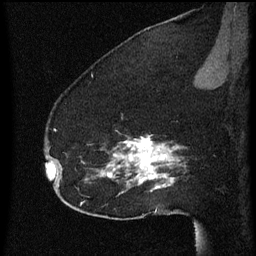
Breast MRI (dynamic contrast-enhanced), one sagittal slice. Slice 45 of 60 in the series (ordered by position). Dynamic contrast-enhanced series, image 2 of 3 at this slice position (ordered by acquisition). 1.5 T. TE 4.2 ms, TR 8 ms. 256 × 256 image matrix, field of view 180 × 180 mm. Female patient, age 52 years.
Outlined on this slice (semi-automatic segmentation, software-assisted and operator-edited):
- analysis volume of interest (the breast-tissue region the enhancement analysis was run in; not a lesion): bounding box <54,118,178,207> (left, top, right, bottom; pixels)
- tumour enhancement mask (voxels above the 70 % enhancement threshold inside the analysis volume of interest): <54,130,178,189>